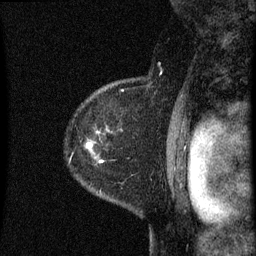
Breast MRI (dynamic contrast-enhanced), one sagittal slice; dynamic contrast-enhanced series, image 2 of 3 at this slice position (ordered by acquisition); 1.5 T; TE 4.2 ms, TR 8 ms; 2 mm slice thickness; 256 × 256 image matrix, field of view 180 × 180 mm. Patient: female, 60 years.
Structures marked on this image (semi-automatically segmented with operator editing):
- analysis volume of interest (the breast-tissue region the enhancement analysis was run in; not a lesion): bounding box <71,82,126,163> (left, top, right, bottom; pixels)
- tumour enhancement mask (voxels above the 70 % enhancement threshold inside the analysis volume of interest): <87,142,92,147>